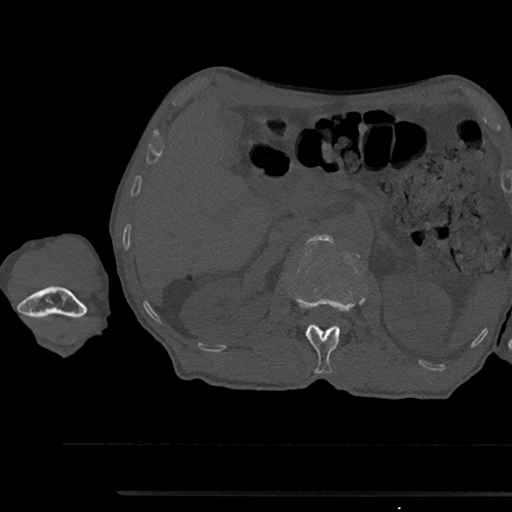
CT including the spine, one axial slice. Slice 618 of 797 in the series (ordered by position). Reconstruction kernel Br40s/3. 120 kVp. Bone window (W 1800 / L 400 HU). 0.5 mm slice thickness. 512 × 512 image matrix, field of view 367 × 367 mm. Male patient, age 79 years. Case-level facts recorded for this patient, not image findings: primary cancer: prostate.
Outlined on this slice (semi-automatic segmentation, software-assisted and operator-edited):
- L1 vertebra: bounding box <294,295,363,374> (left, top, right, bottom; pixels)
- L2 vertebra: <307,234,335,244>